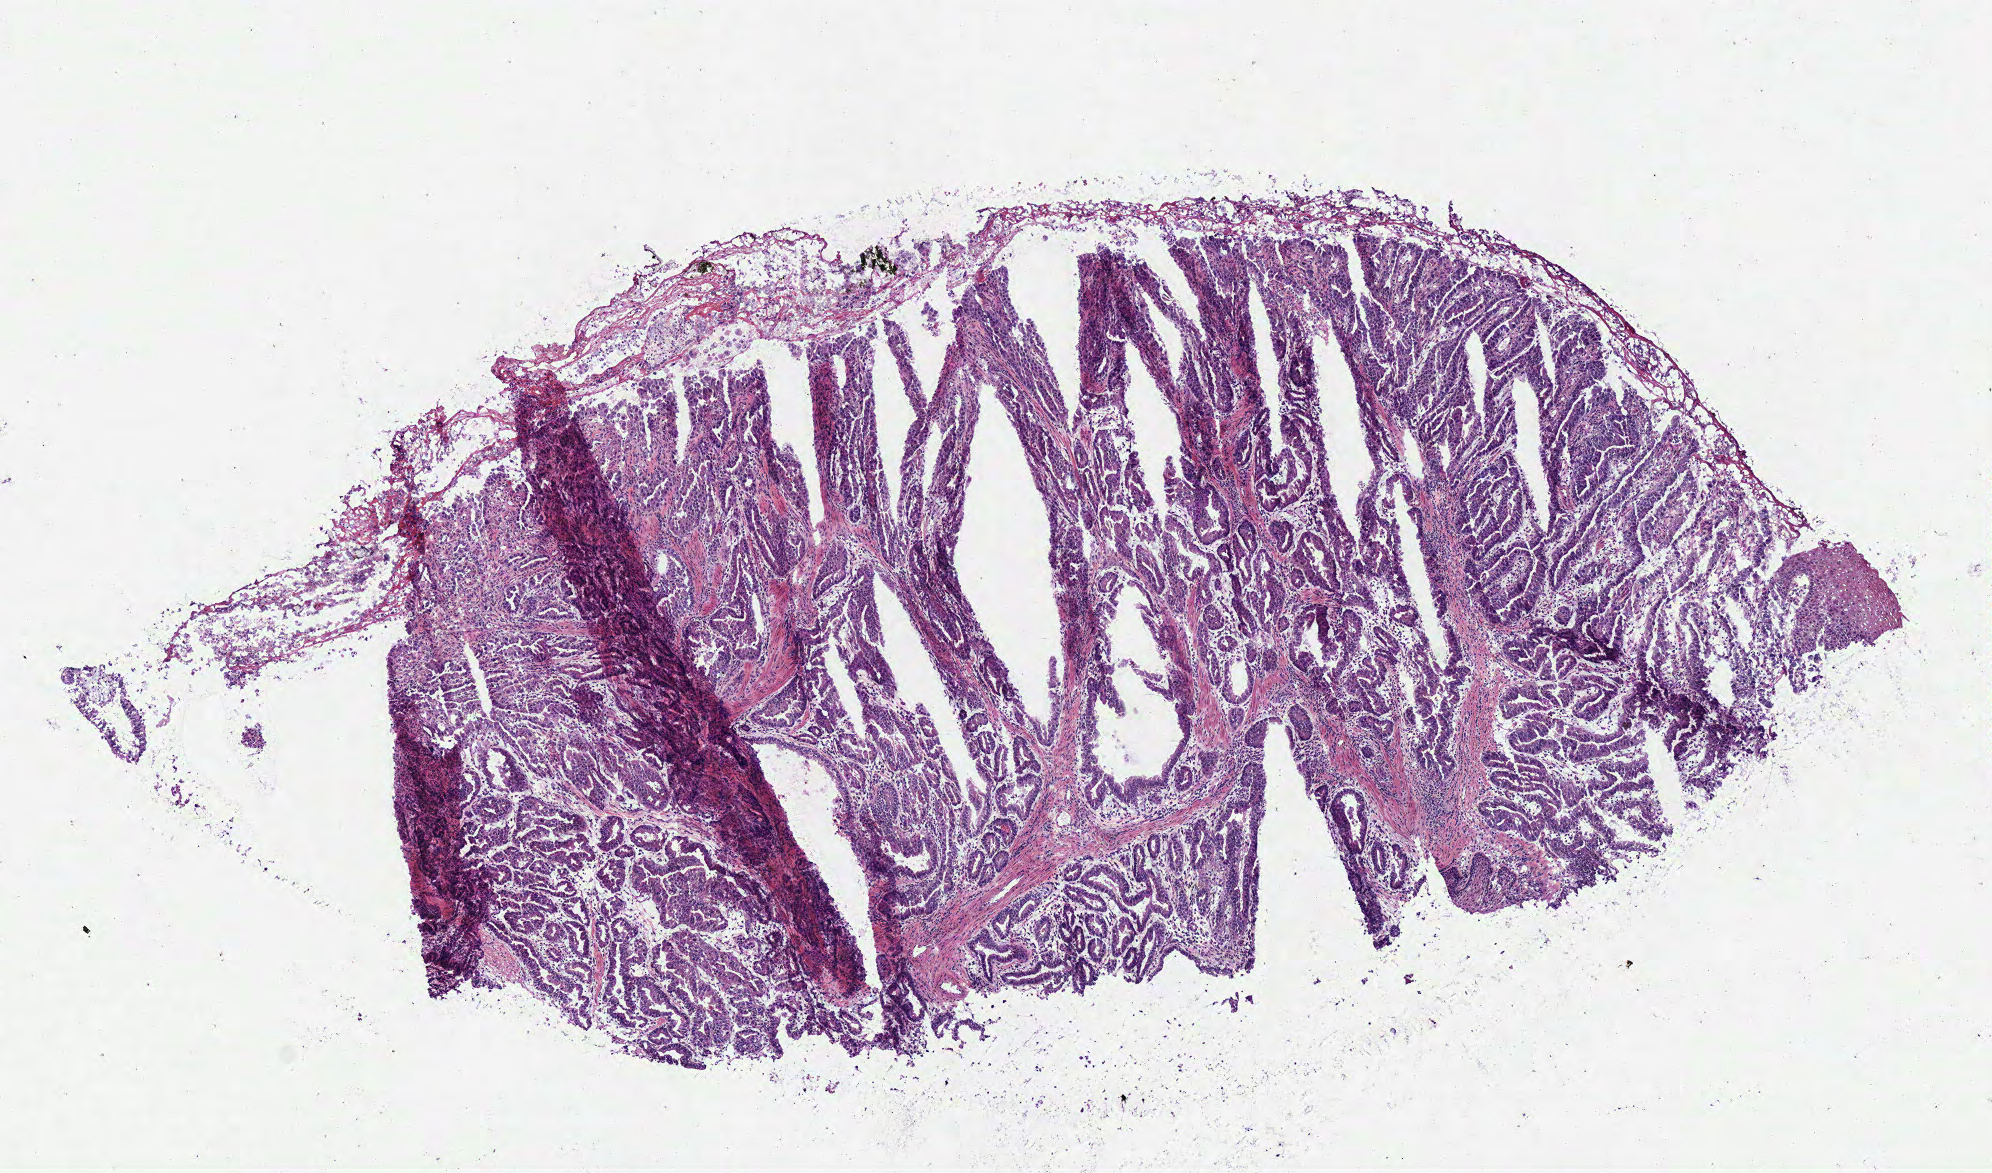
Hematoxylin and eosin (H&E) stained whole-slide image — a low-resolution overview of the entire scanned area, about 7.8 x 4.6 mm (acquisition: 40x scan). Frozen section from the bottom of the tissue portion. Stomach, primary tumour sample. Male patient; age at initial diagnosis 62 years. Histologic grade: G2 (moderately differentiated). Composition of this section per pathologist review: tumour cells 82%, tumour nuclei 75%, normal cells 3%, stromal cells 15%, necrosis 0%.
• AJCC pathologic stage: II (6th edition)
• pathologic diagnosis: Papillary adenocarcinoma, NOS (cardia, NOS)
• TNM: T2 N1 M0